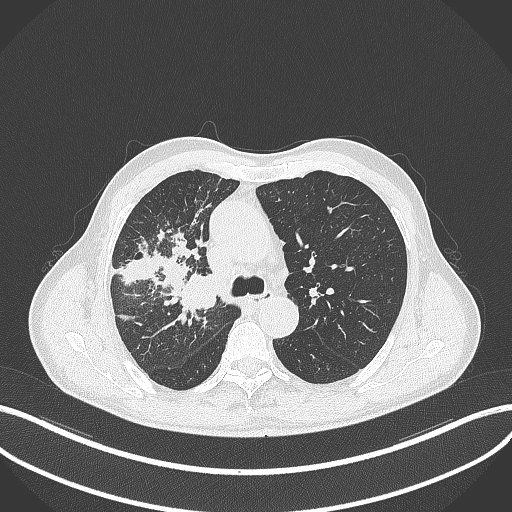
Chest CT, one axial slice; position 329 of 490 along the scan axis; 120 kVp; lung window (W 1500 / L -600 HU); 1 mm slice thickness; 512 × 512 image matrix. Patient: male, 69 years. Case-level facts recorded for this patient, not image findings: clinical TNM (as recorded): T2a N0 M0.
Outlined on this slice (rectangle marked by the reading radiologist):
- lung tumour (recorded histology: adenocarcinoma): bounding box [x1, y1, x2, y2] px = [182, 272, 223, 311]